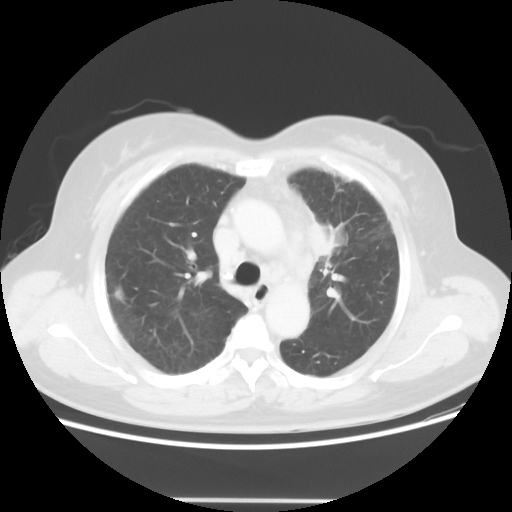
Chest CT, one axial slice. Slice 38 of 52 in the series (ordered by position). Reconstruction kernel STANDARD. Lung window (W 1500 / L -600 HU). 5 mm slice thickness. 512 × 512 image matrix, field of view 382 × 382 mm. Female patient, age 52 years. Case-level facts recorded for this patient, not image findings: clinical TNM (as recorded): T2 N3 M0.
Outlined on this slice (rectangle marked by the reading radiologist):
- lung tumour (recorded histology: adenocarcinoma): box from (x=298, y=205) to (x=353, y=267) px